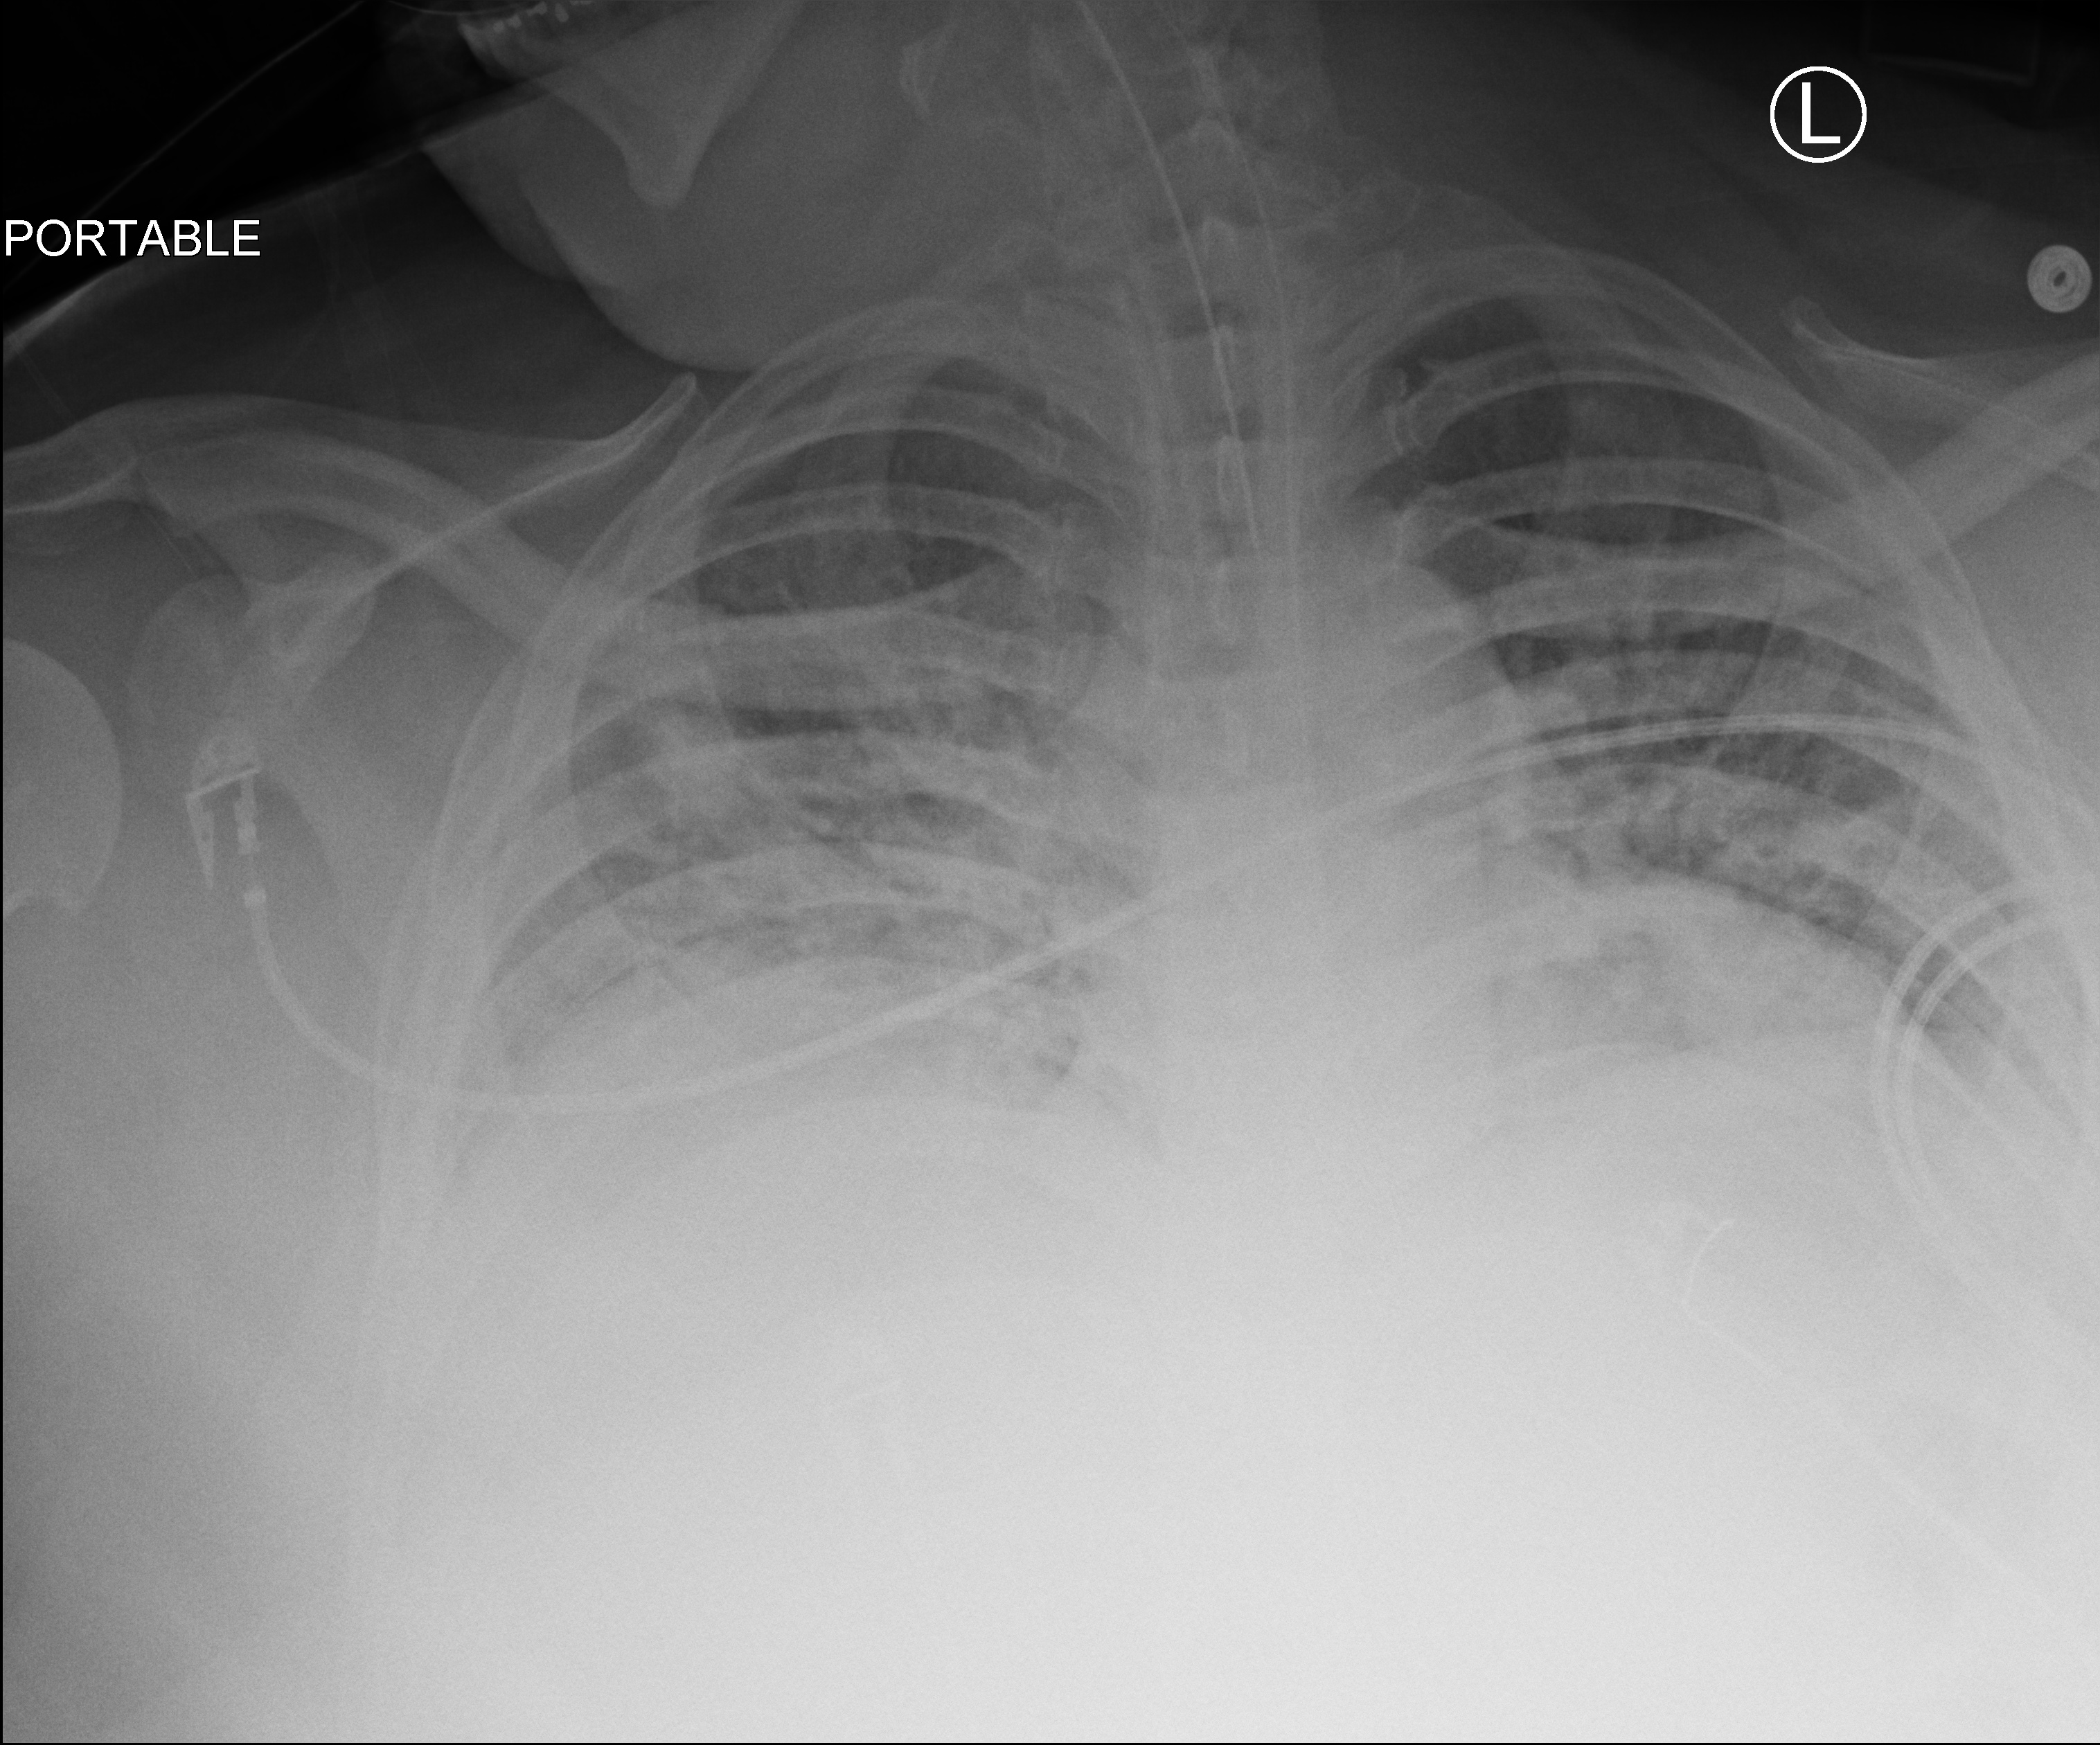
Portable chest radiograph, anteroposterior (AP) projection. Patient hospitalised with COVID-19; male, aged 18–59 years.
From the hospital-stay record, not from the radiograph (when in the stay this image was taken is not recorded): admitted to intensive care during this hospital stay: yes; mechanically ventilated during this hospital stay: yes.